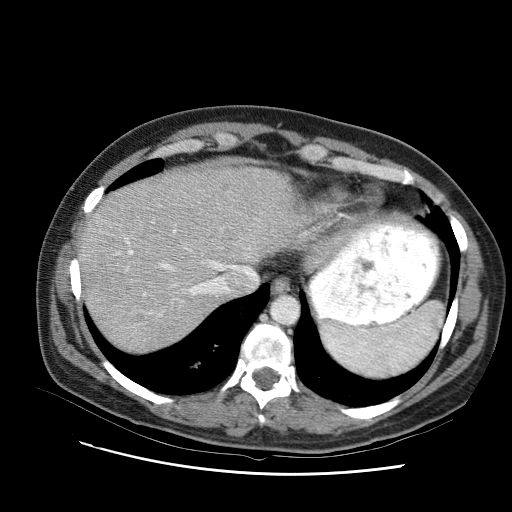
Contrast-enhanced abdominal CT (liver protocol), one axial slice; position 79 of 95 along the scan axis; 120 kVp; one of 2 acquisitions stored at this slice position; soft-tissue window (W 400 / L 40 HU); 512 × 512 image matrix, field of view 360 × 360 mm. From the clinical record (not read from this slice): diagnosis: hepatocellular carcinoma (patient treated with transarterial chemoembolisation; whether this scan precedes or follows treatment is not stated here); TNM stage (as recorded): Stage-I; Child-Pugh class: B; tumour nodularity: uninodular.
Outlined on this slice (semi-automatically segmented with operator editing):
- liver parenchyma outside the tumour (the mass and vessels are separate outlines, so this box may not span the whole liver): bounding box <80,164,288,326> (left, top, right, bottom; pixels)
- liver vessels: <119,213,279,291>